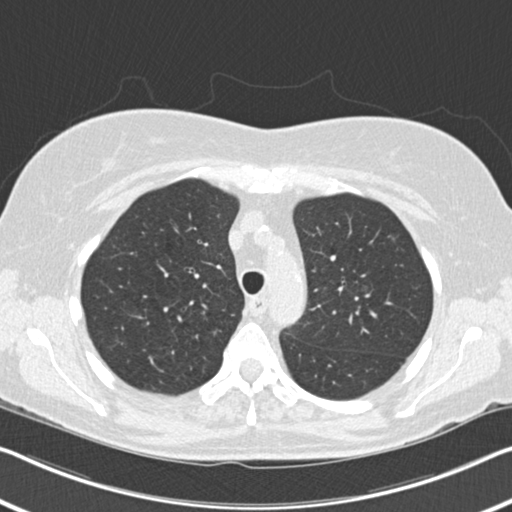
Axial slice from a low-dose chest CT screening exam; second annual screen; lung window (W 1500 / L -600 HU); 2 mm slice thickness; standard (soft-tissue) reconstruction kernel (B30f); 120 kVp; slice 56 of 202 in the series; 512 × 512 image matrix, field of view 336 × 336 mm. Female, age 60 years at enrolment.
Expert-annotated lung lesion, box from (x=380, y=228) to (x=419, y=265) px. The screening reader recorded 6 non-calcified nodules or masses ≥4 mm on this exam (right upper lobe, right middle lobe, right lower lobe, right lower lobe, left lower lobe, lingula); which of them this box marks is not recorded. Official screen result: positive, change unspecified: nodule(s) >= 4 mm or enlarging nodule(s), mass(es), or other non-specific abnormalities suspicious for lung cancer.